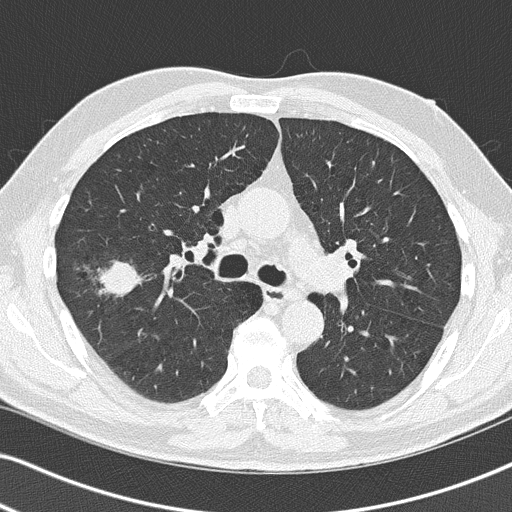
Low-dose screening chest CT, one axial slice. Position 82 of 140 along the scan axis. Reconstruction kernel B50f. 120 kVp. Lung window (W 1500 / L -600 HU). 512 × 512 image matrix, field of view 330 × 330 mm.
Annotated regions visible in this slice (outlined manually by an expert reader):
- lesion 1 (tumor, upper lobe of right lung): bounding box [x1, y1, x2, y2] px = [98, 261, 141, 297]